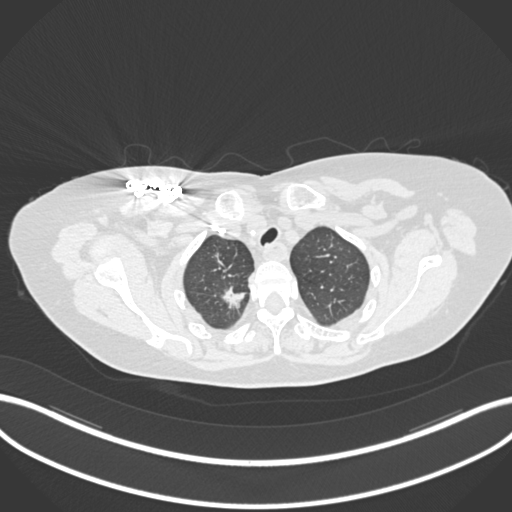
Chest CT, one axial slice; position 154 of 176 along the scan axis; reconstruction kernel B30f; 120 kVp; lung window (W 1500 / L -600 HU); 1 mm slice thickness; 512 × 512 image matrix, field of view 400 × 400 mm. Patient: female, 72 years. From the clinical record (not read from this slice): clinical TNM (as recorded): T1c N0 M0.
Structures marked on this image (bounding box drawn by a radiologist):
- lung tumour (recorded histology: adenocarcinoma): bounding box [x1, y1, x2, y2] px = [215, 285, 248, 314]